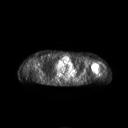
FDG PET of an extremity soft-tissue mass (from a PET/CT study), one axial slice. Slice 183 of 267 in the series (ordered by position). 3.27 mm slice thickness. 128 × 128 image matrix, field of view 700 × 700 mm. Female patient, age 83 years. From the clinical record (not read from this slice): histological type: pleiomorphic leiomyosarcoma; grade: high; site of the primary tumour: left biceps.
Annotated regions visible in this slice (expert contour drawn on MRI and transferred to this co-registered scan by the dataset authors):
- gross tumour volume including surrounding oedema: bounding box (x1, y1, x2, y2) in pixels: (91, 63, 99, 73)
- gross tumour volume (mass): (91, 63, 98, 71)